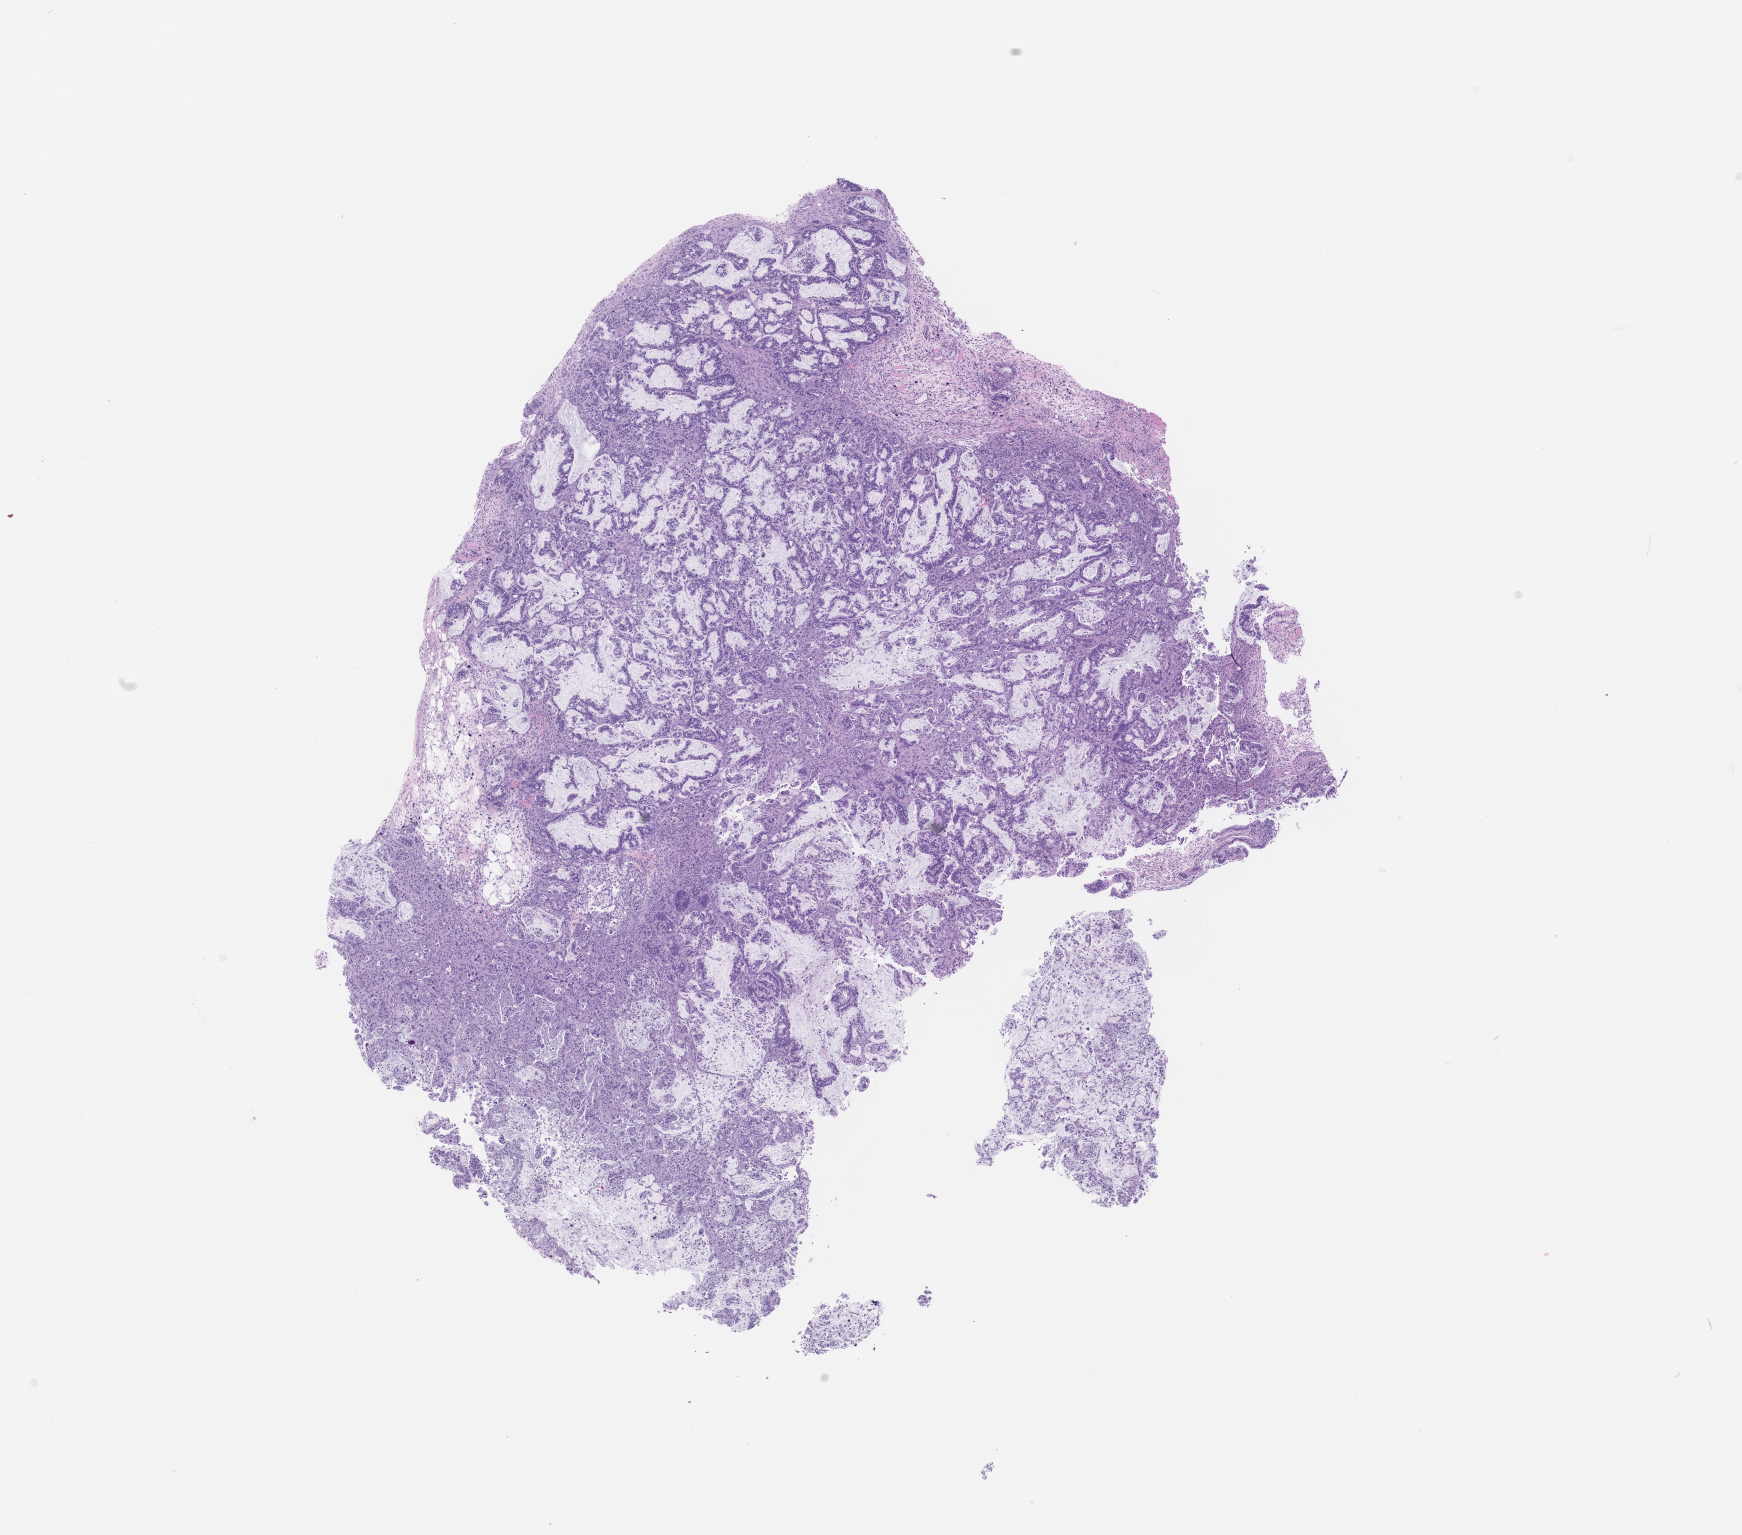
Hematoxylin and eosin (H&E) whole-slide image of a patient-derived xenograft (PDX) tumor grown in a mouse, passage 0, whole scanned area (about 14.0 x 12.3 mm) shown as a low-resolution overview. FFPE section. Originating tumor site category: pancreas.
Originating patient diagnosis: Pancreatic Adenocarcinoma.